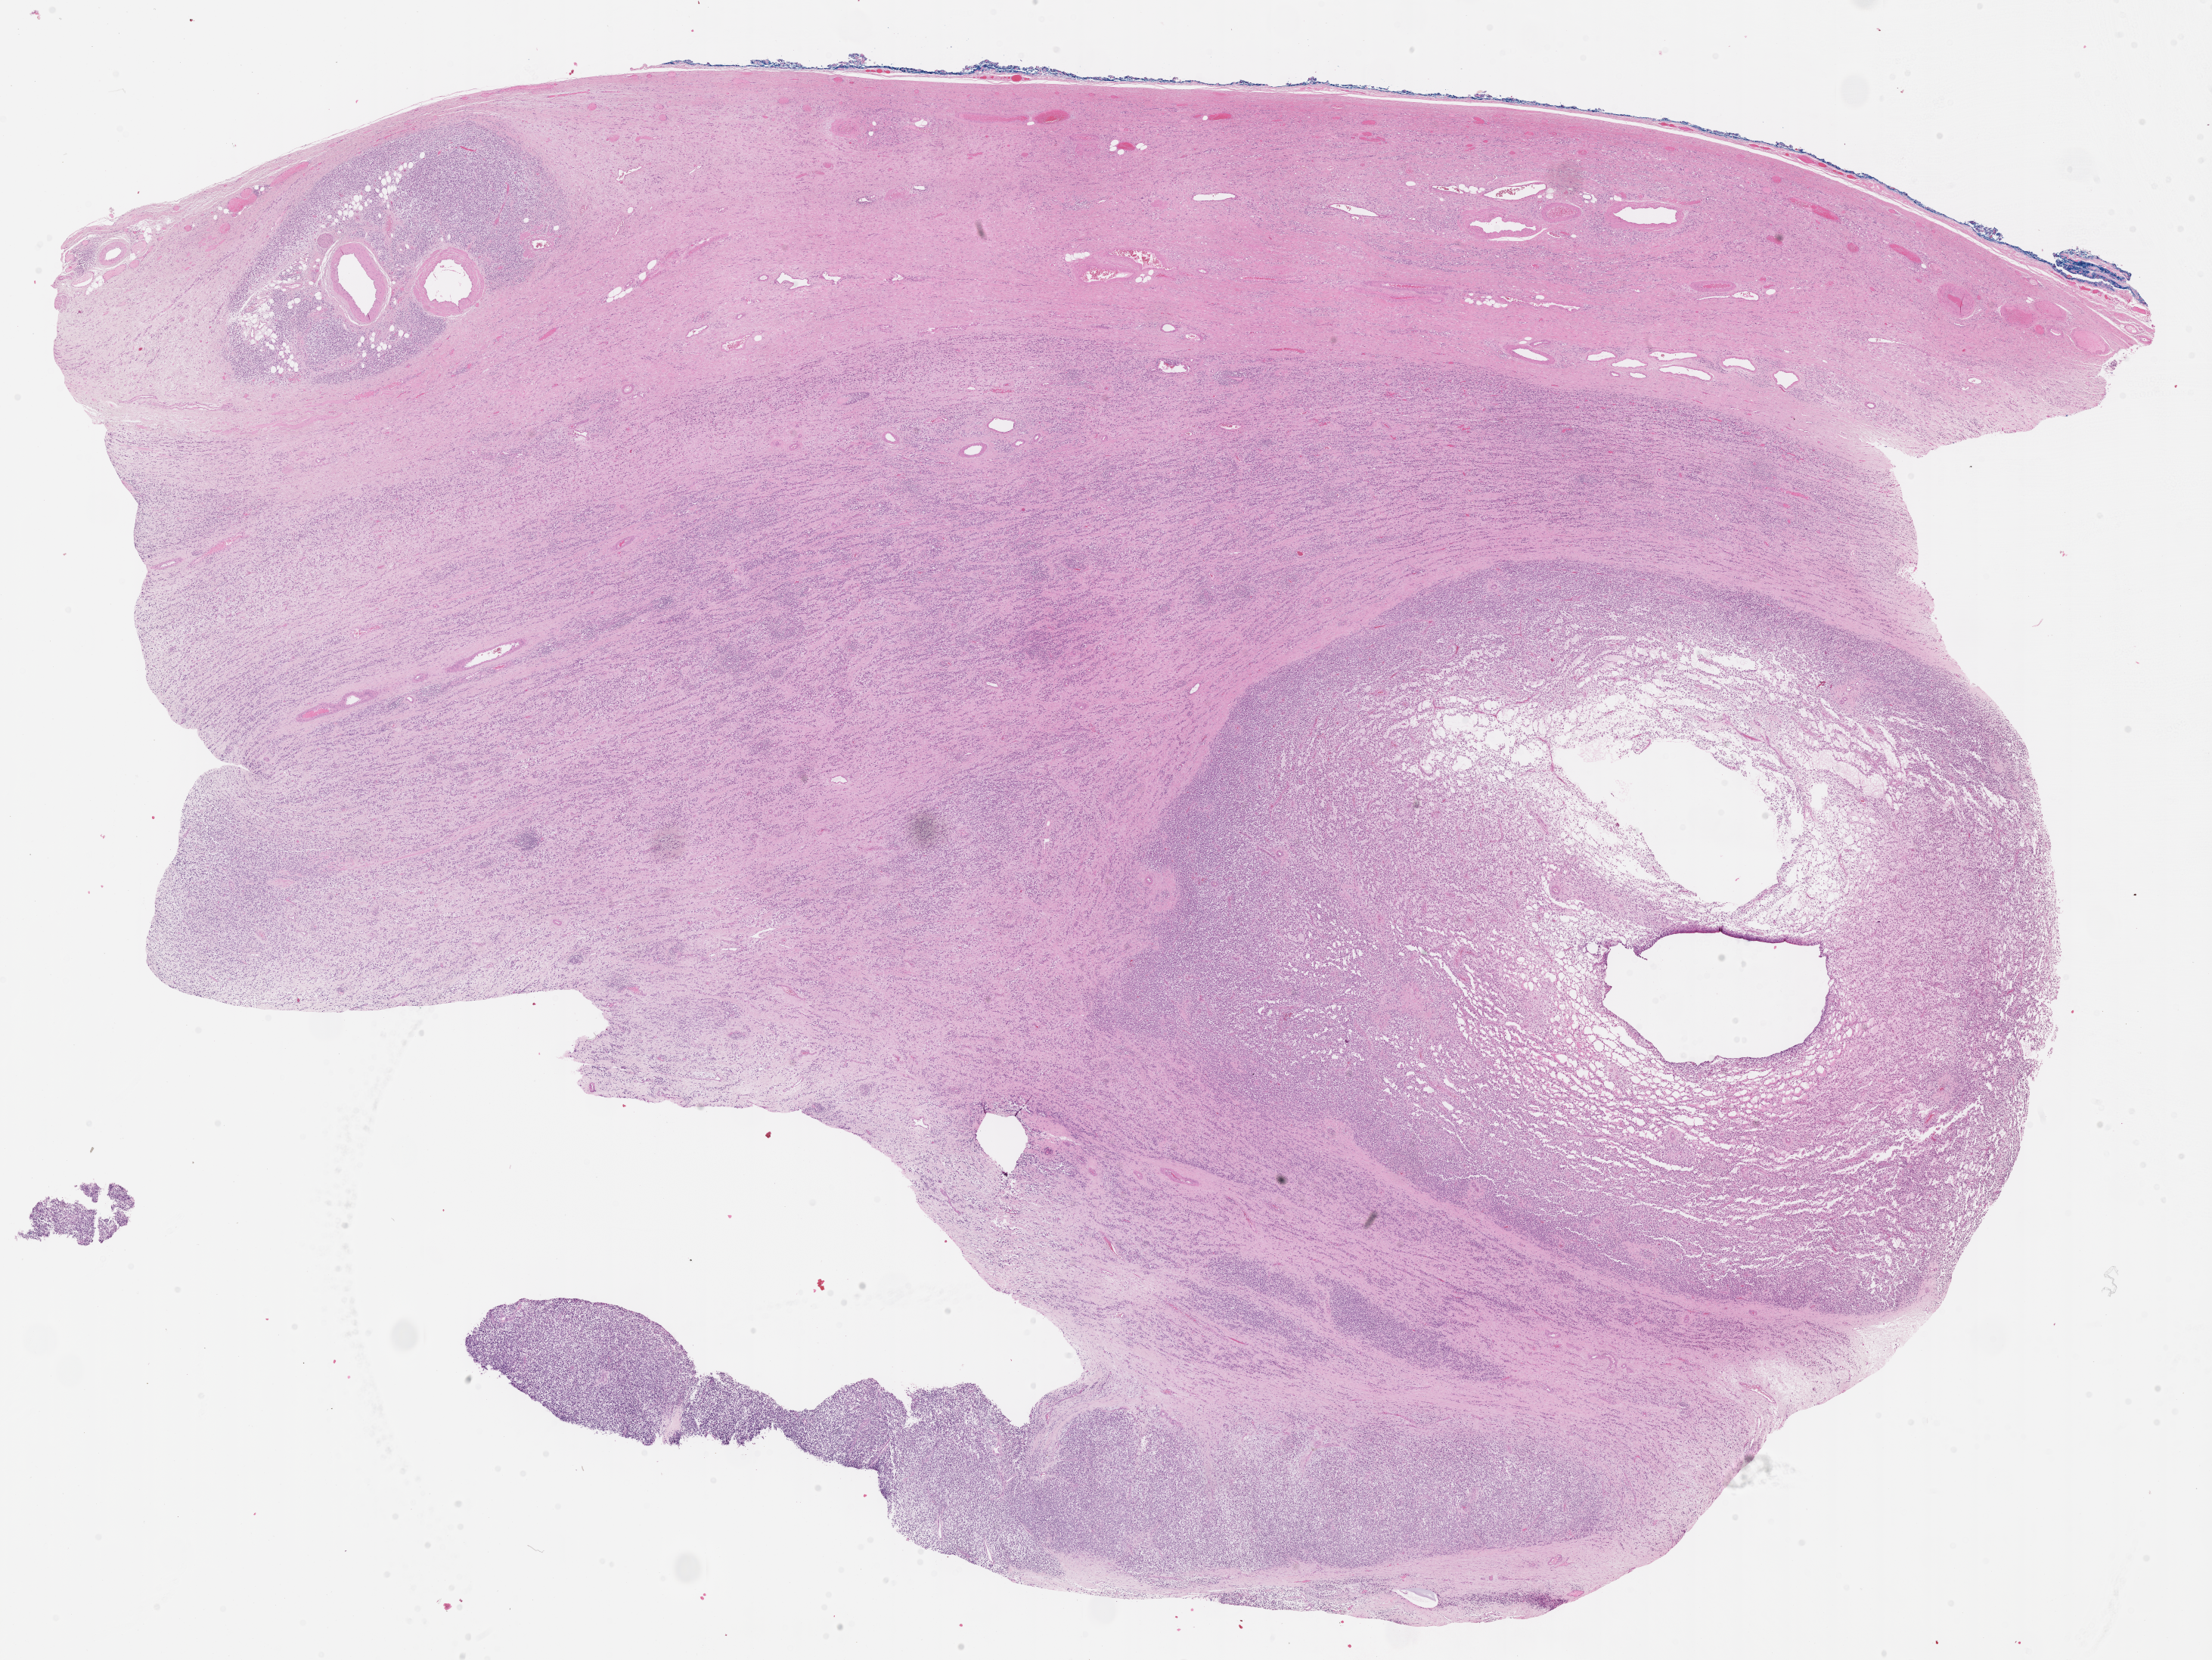
Whole-slide image, H&E stain of tumor tissue, a low-resolution overview of the entire scanned area, about 23.6 x 17.7 mm. Formalin-fixed, paraffin-embedded (FFPE) tissue. Sample anatomic site: testicle, left. Patient: male, age 18.4 years at diagnosis.
Metastatic status at presentation (as recorded): non-metastatic (unconfirmed). Diagnosis: rhabdomyosarcoma; histological classification: embryonal rhabdomyosarcoma. Primary site (case record): testis-paratesticular. Stage (as recorded): 1.